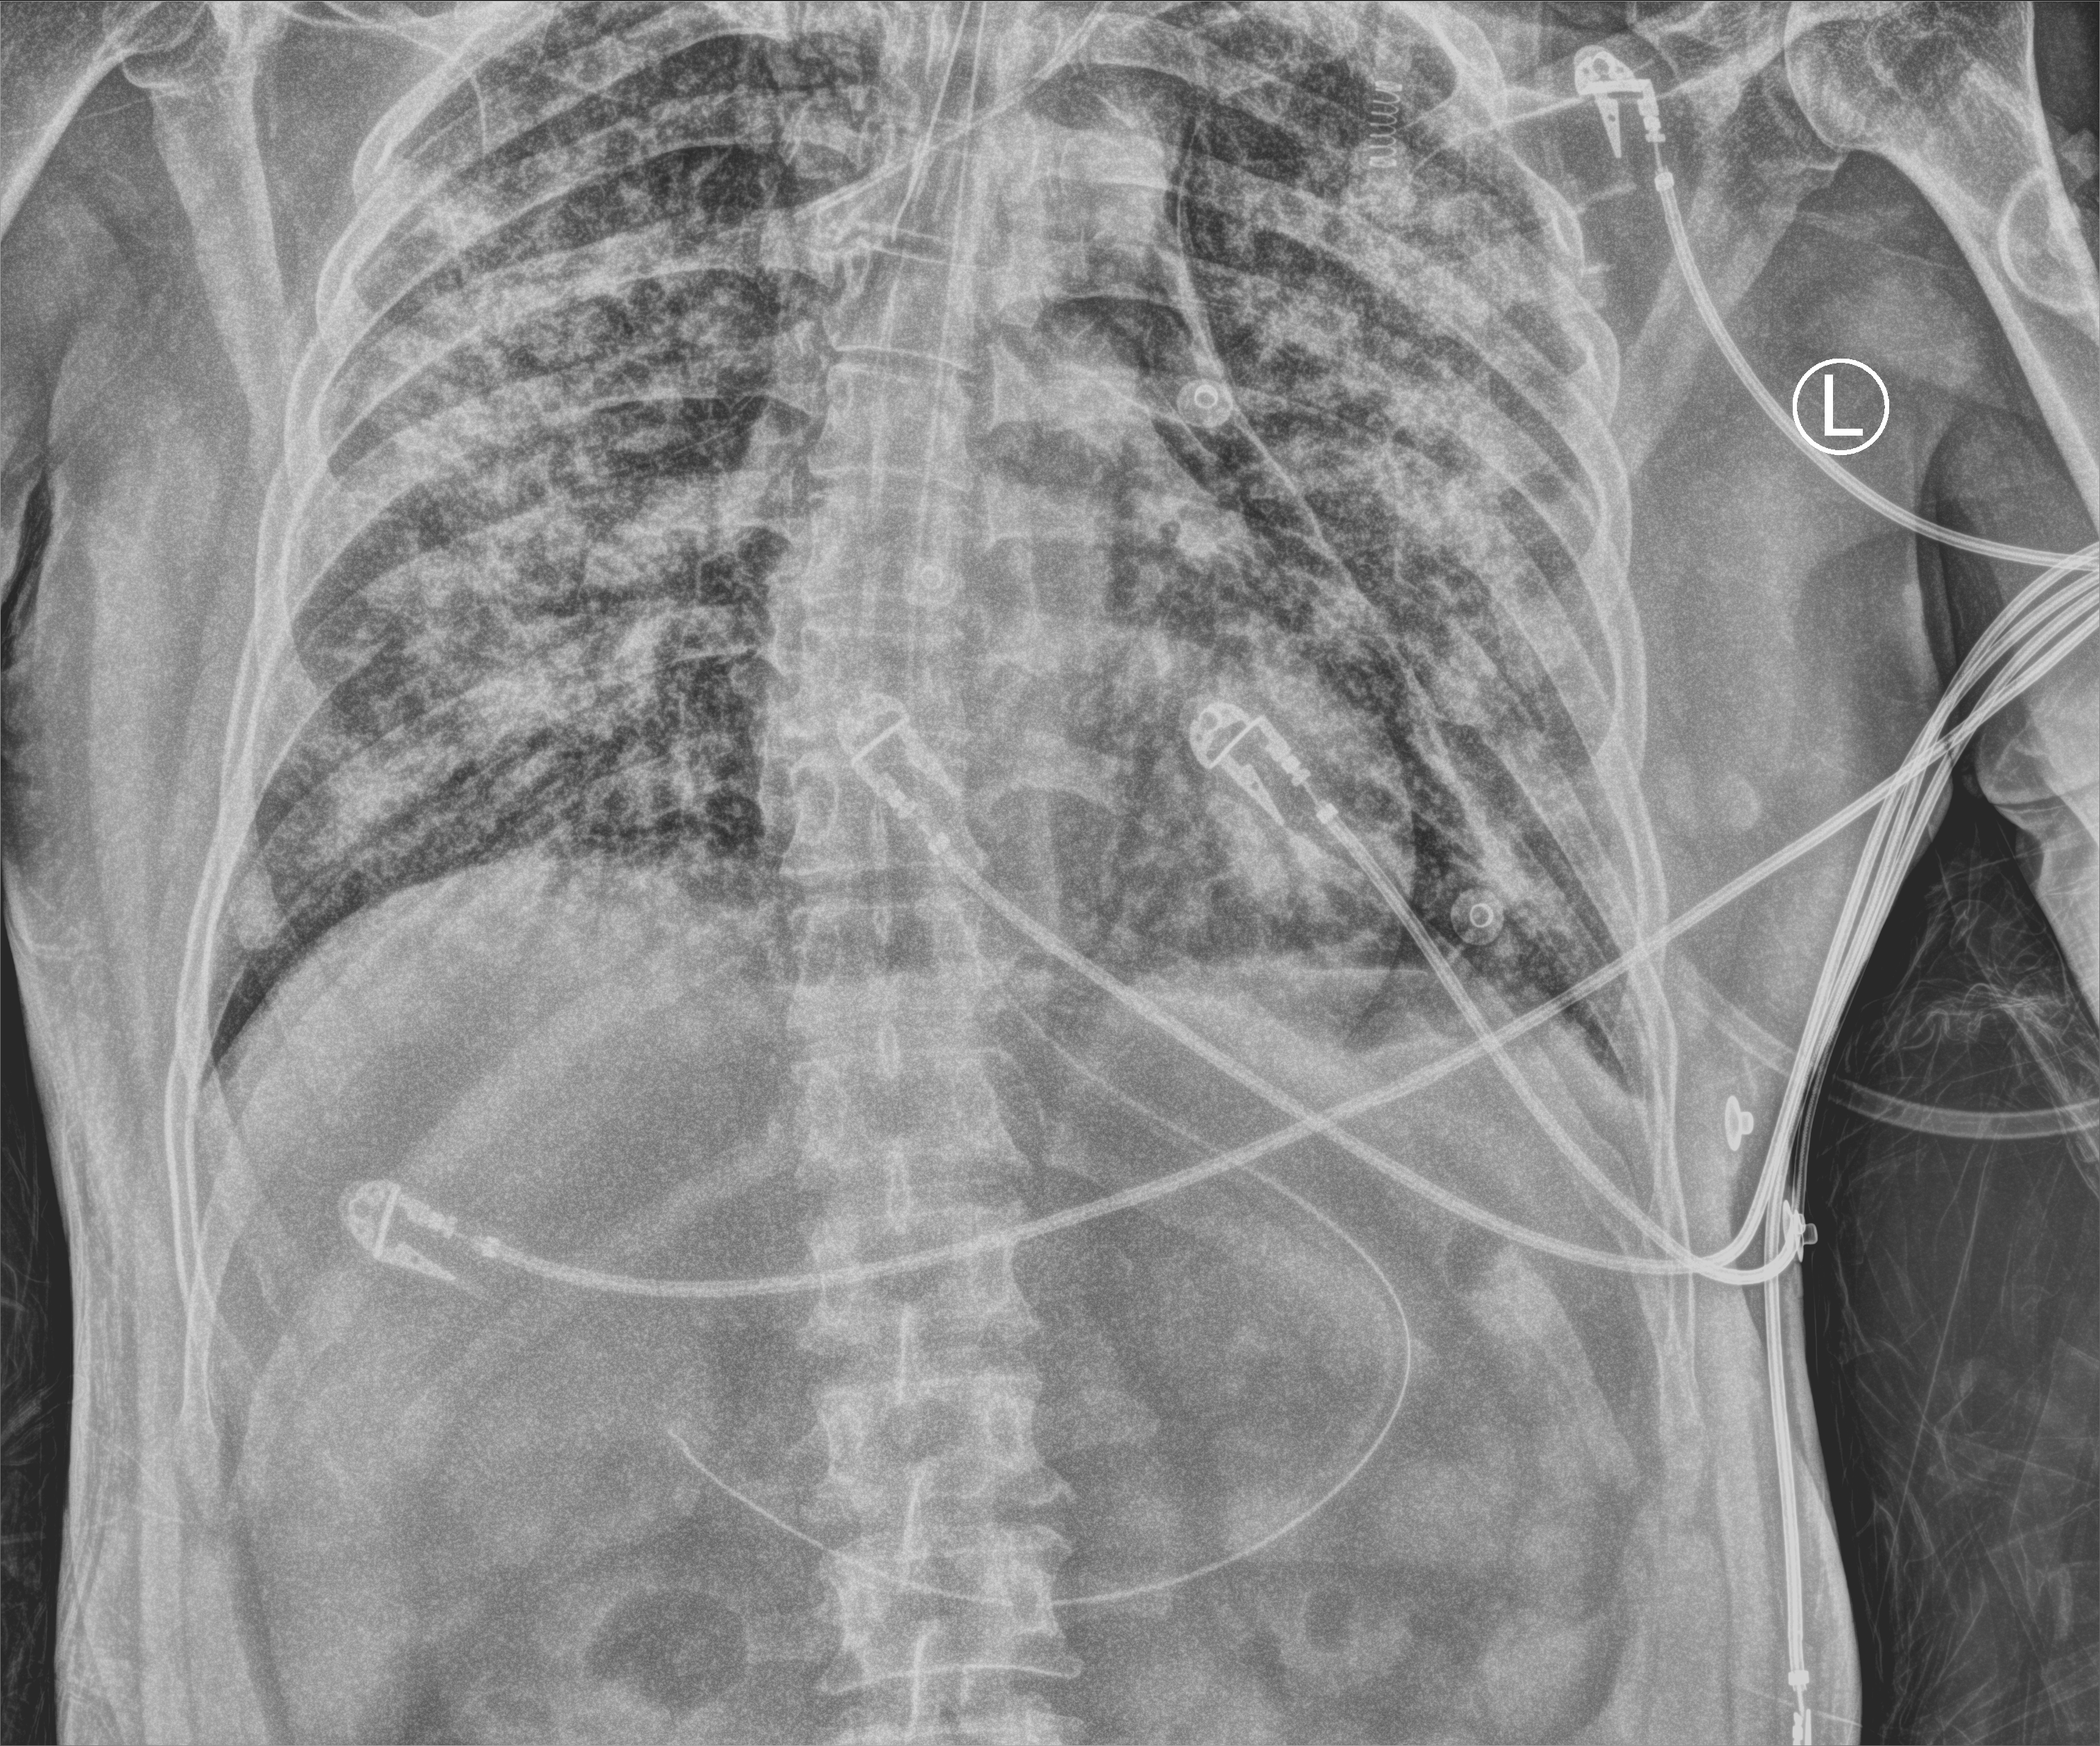
Bedside chest radiograph (computed radiography). Patient hospitalised with COVID-19; male, aged 60–74 years.
Admission-level facts for this patient (not findings on this image; timing relative to this image not recorded): other chronic lung disease (admission record): yes; admitted to intensive care during this hospital stay: yes.